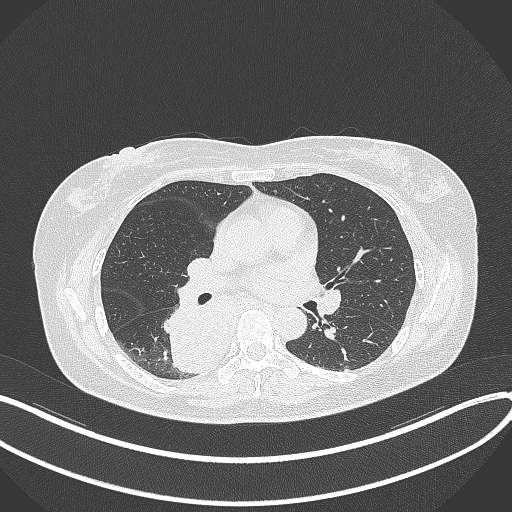
Chest CT, one axial slice; position 196 of 331 along the scan axis; reconstruction kernel B70f; lung window (W 1500 / L -600 HU); 1 mm slice thickness; 512 × 512 image matrix, field of view 400 × 400 mm. Female patient, age 54 years. From the clinical record (not read from this slice): clinical TNM (as recorded): T4 N0 M0.
Outlined on this slice (rectangle marked by the reading radiologist):
- lung tumour (recorded histology: adenocarcinoma): box from (x=158, y=304) to (x=240, y=372) px